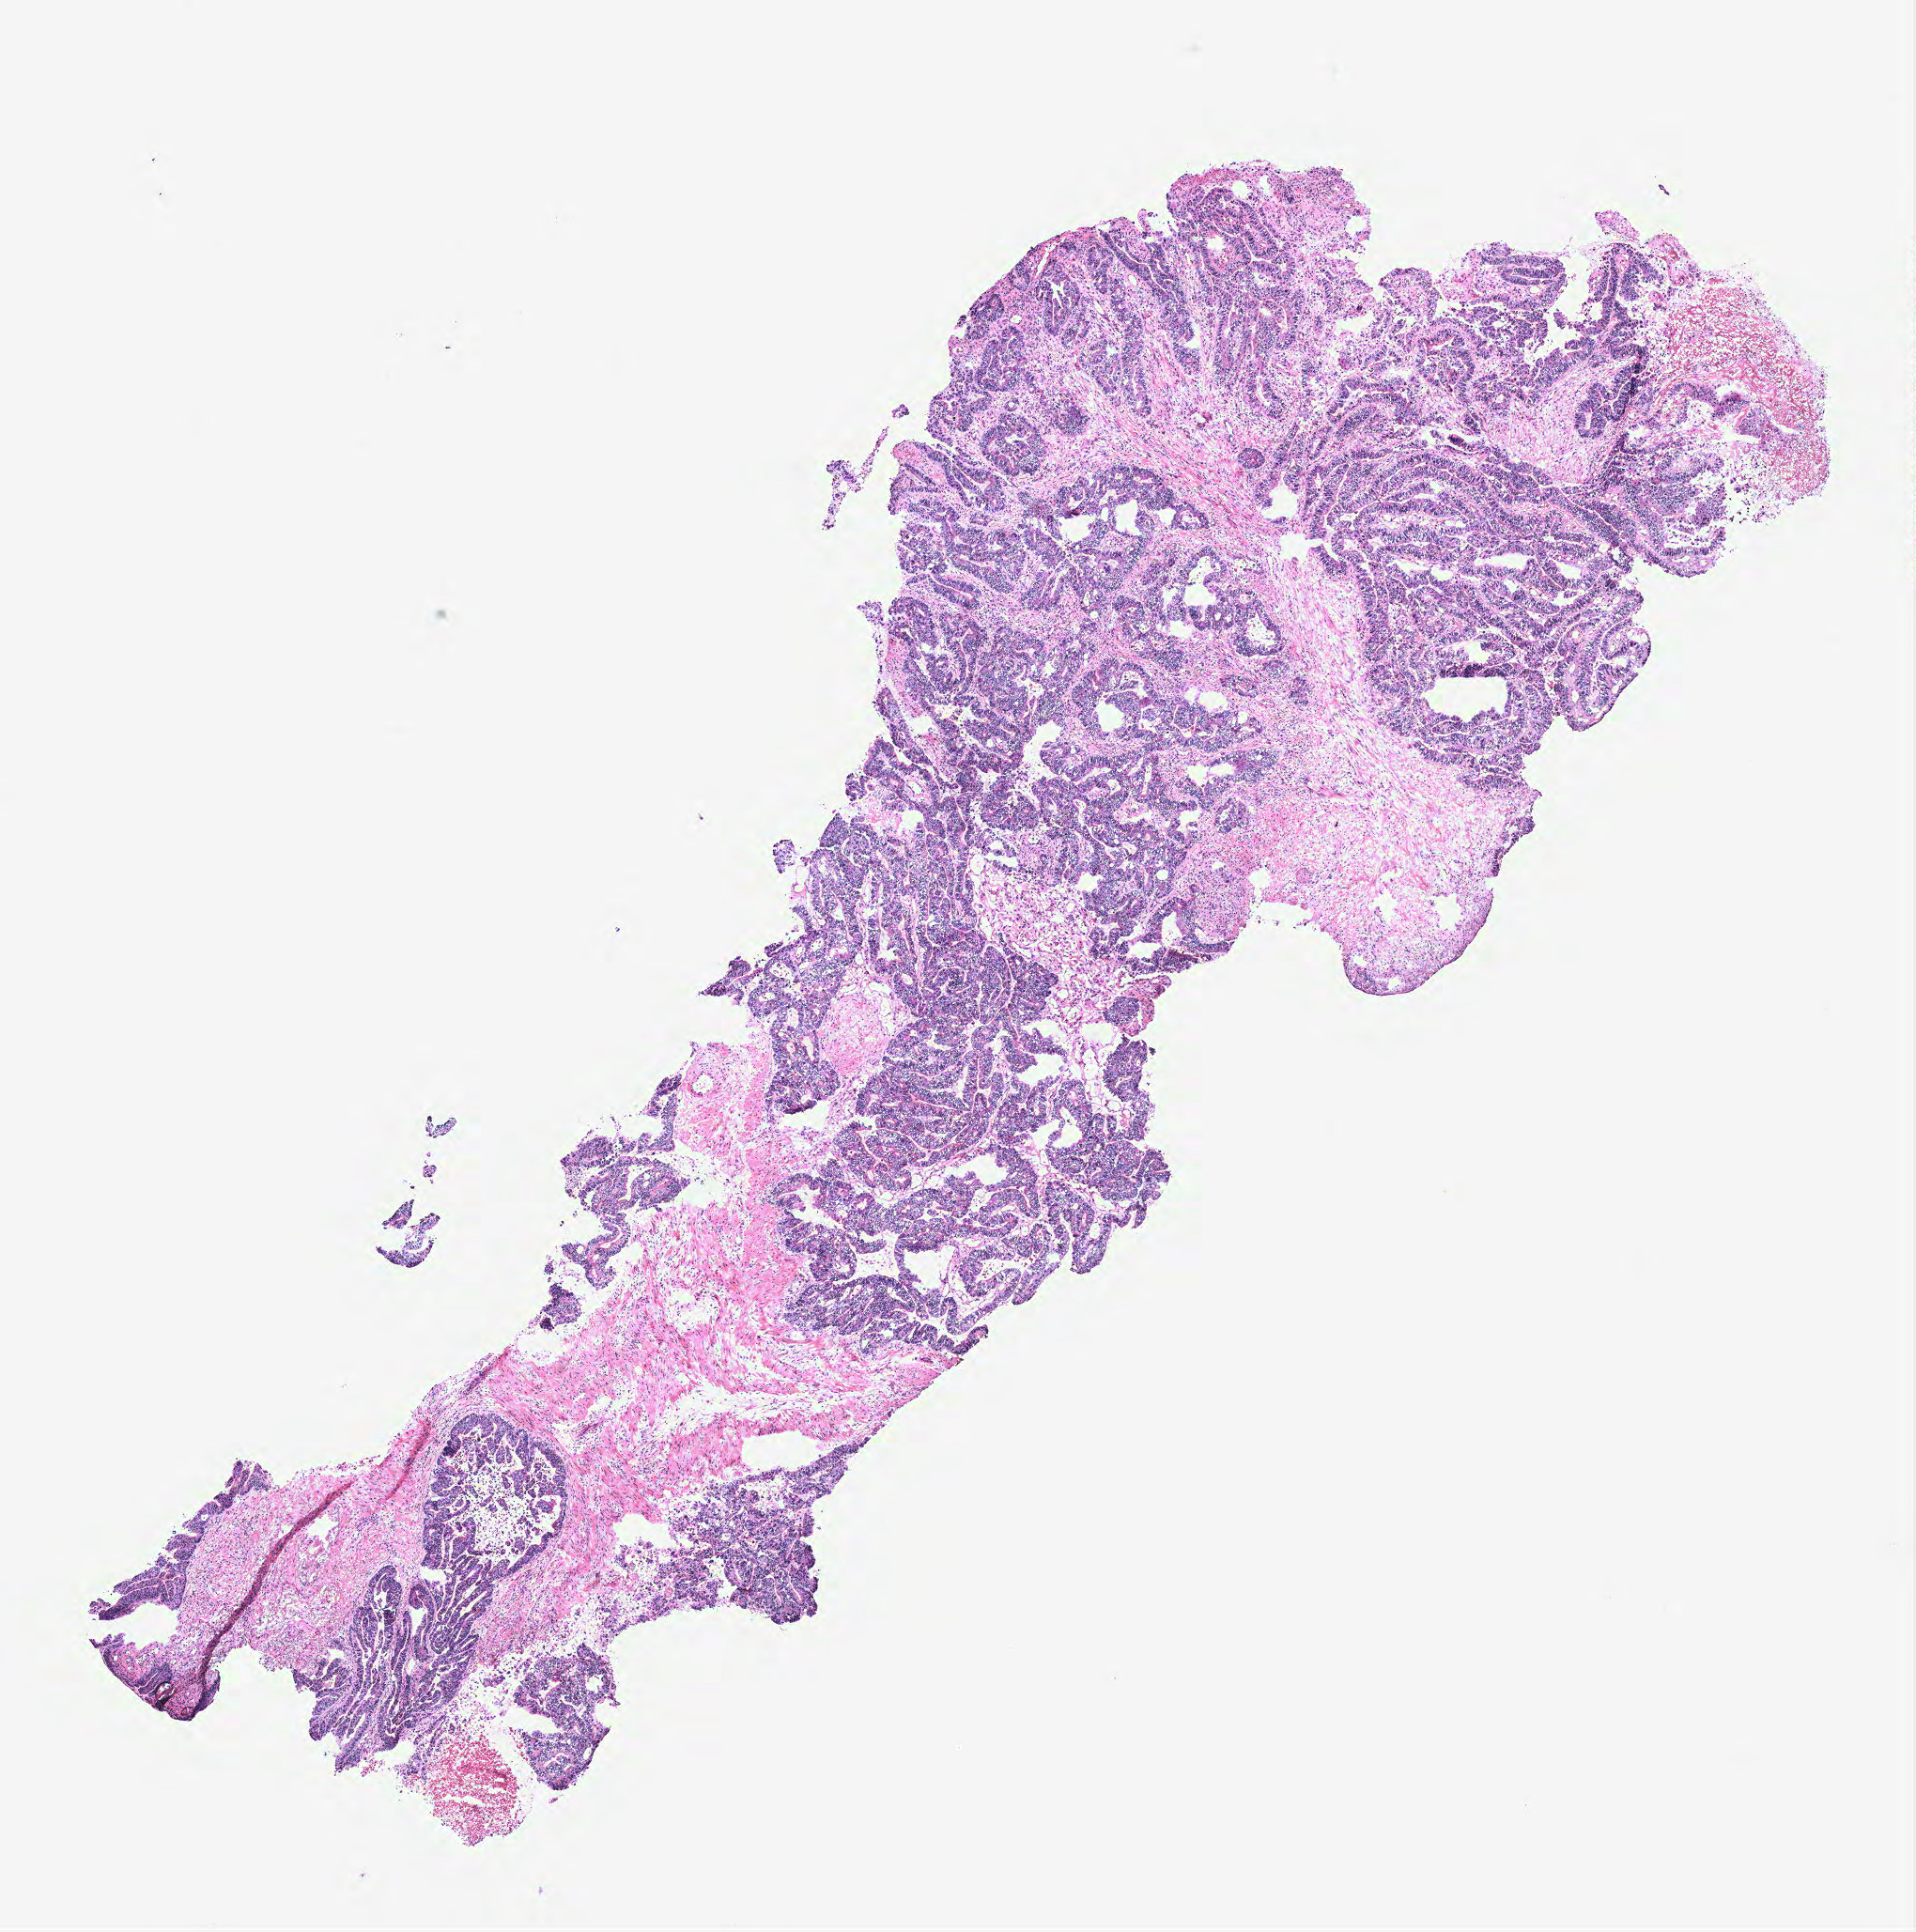
Digitized H&E-stained tissue section (whole slide), whole scanned area (about 8.2 x 8.2 mm) shown as a low-resolution overview, colon, tissue type not recorded.
Patient diagnosis (cohort enrolment): colon cancer (colon).